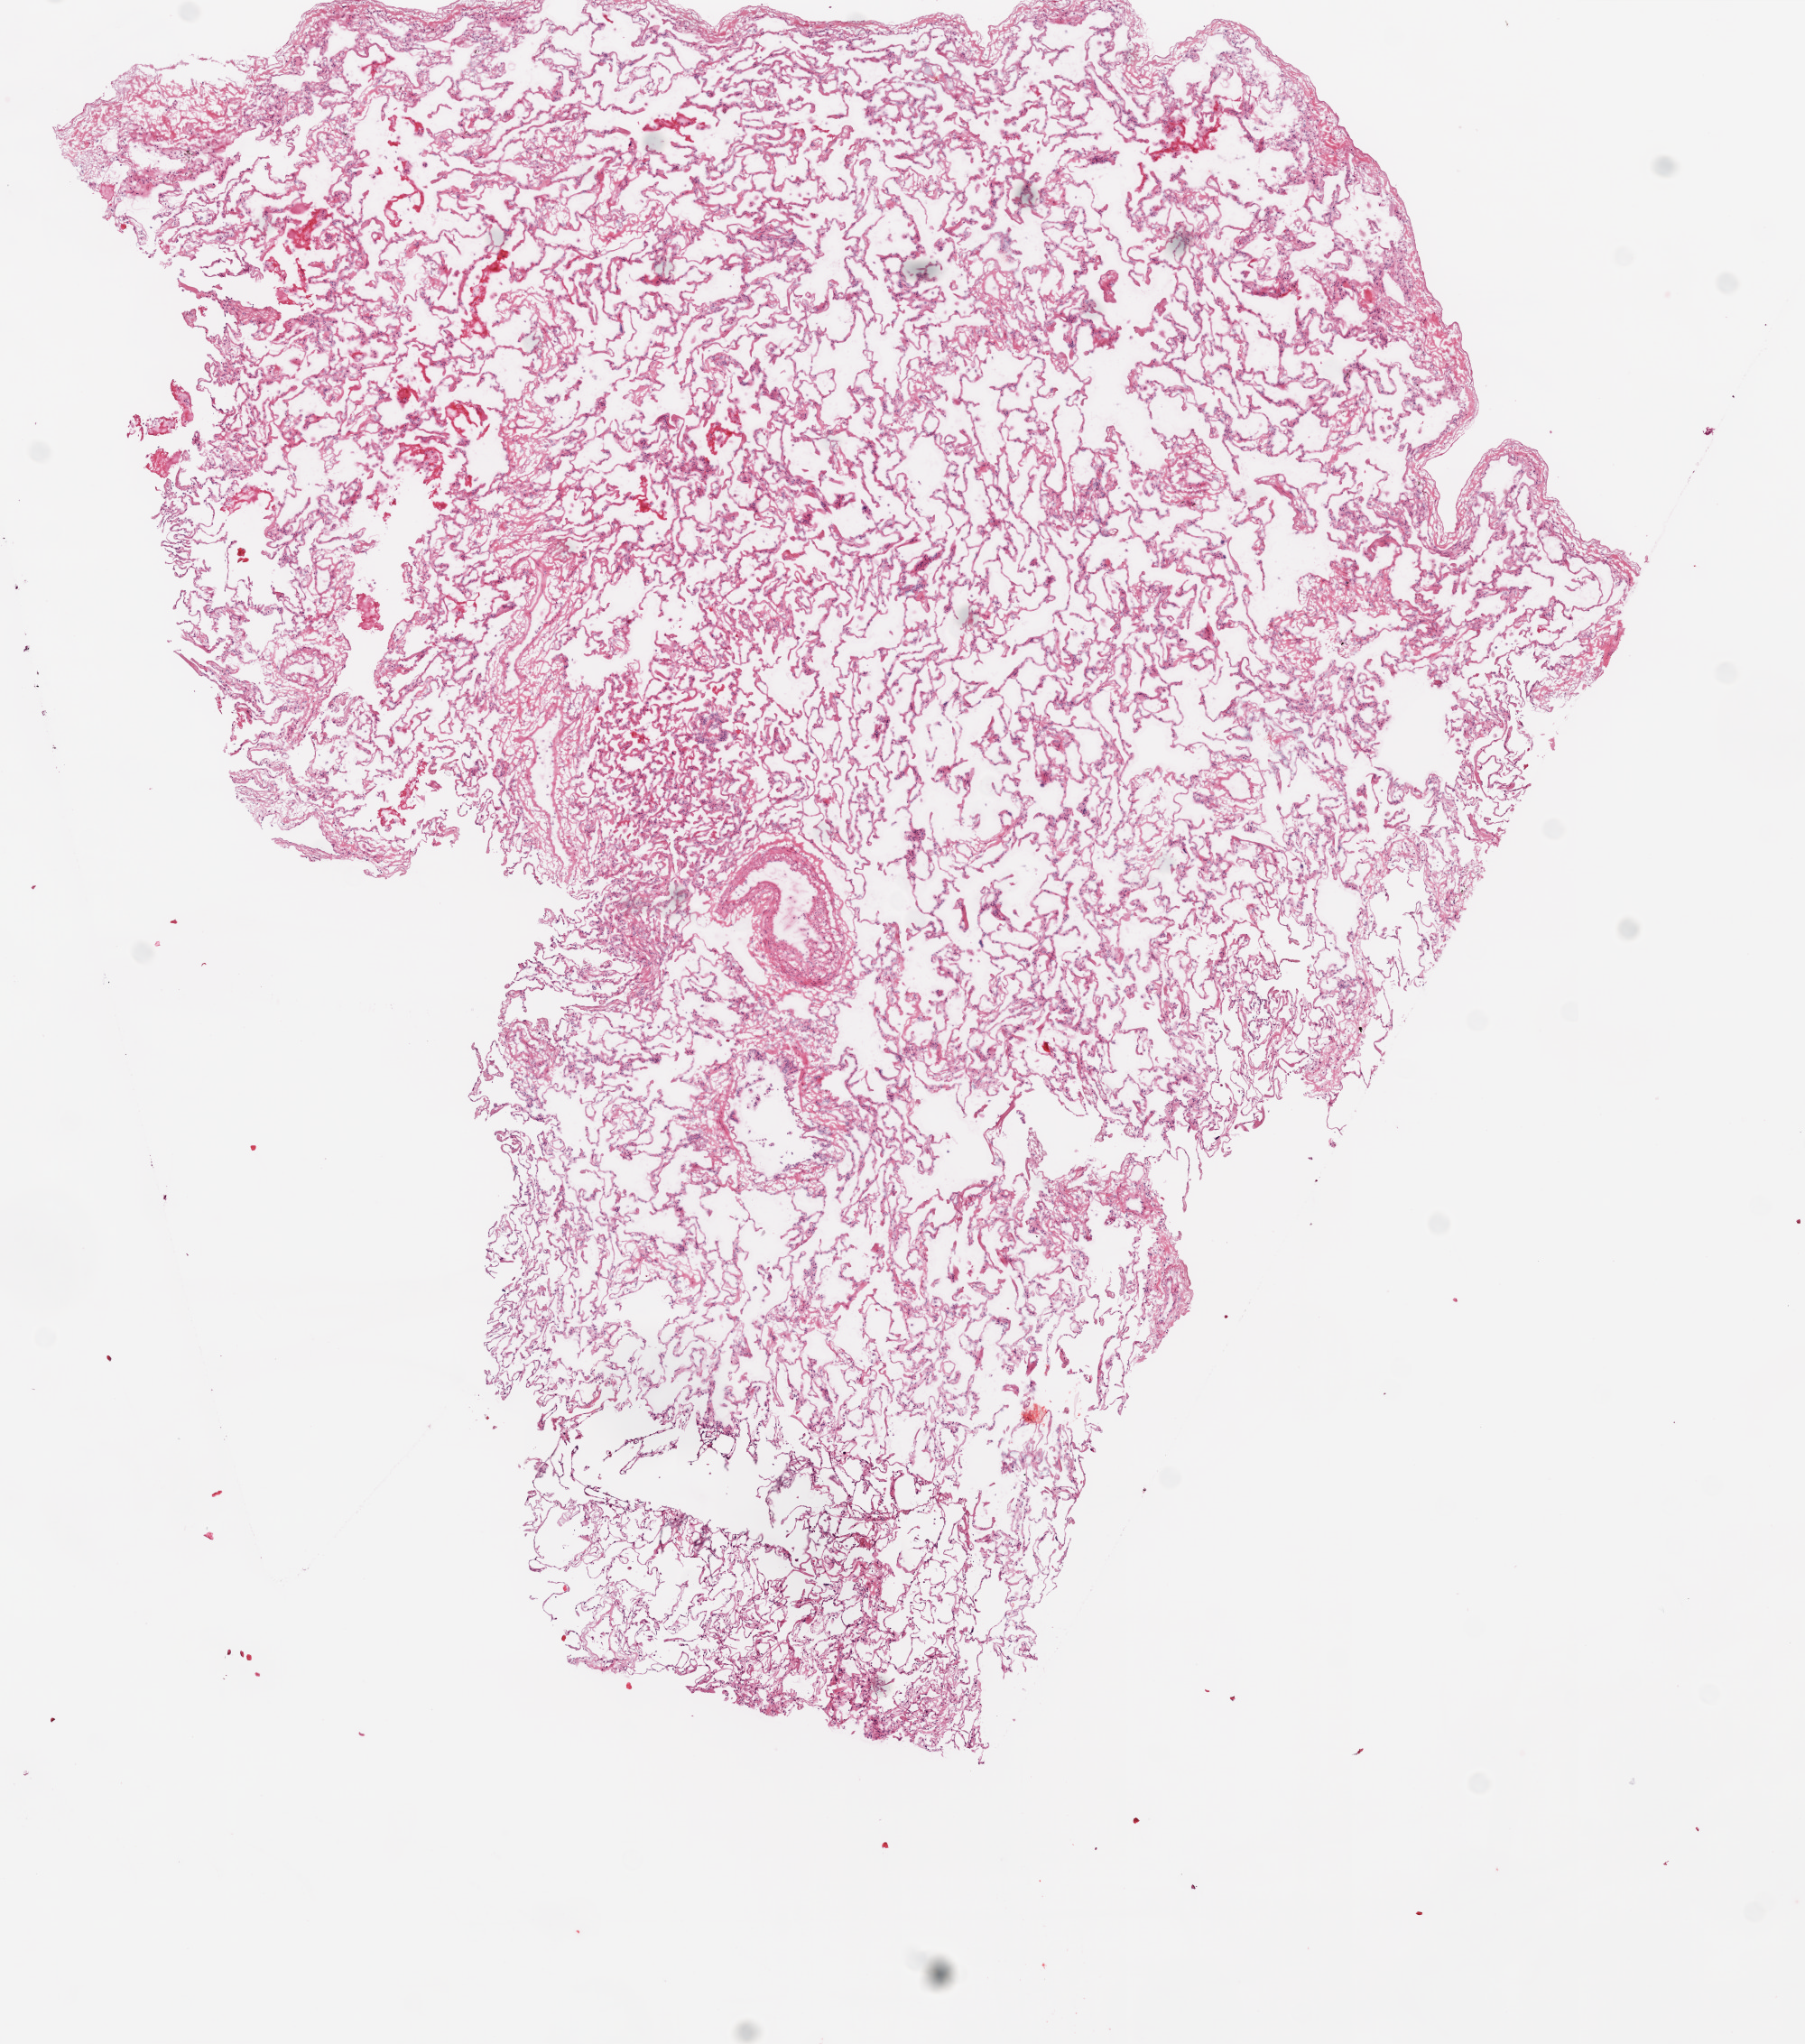
Hematoxylin and eosin (H&E) stained whole-slide image, whole scanned area (about 8.0 x 9.1 mm, slide scanned at 20x) shown as a low-resolution overview; frozen section from the top of the tissue portion; solid tissue normal (non-tumour tissue) sample from the lung. Female, age 78 years at initial diagnosis.
This section: solid tissue normal sample (biorepository sample class). Patient diagnosis: Squamous cell carcinoma, large cell, nonkeratinizing, NOS (upper lobe, lung).